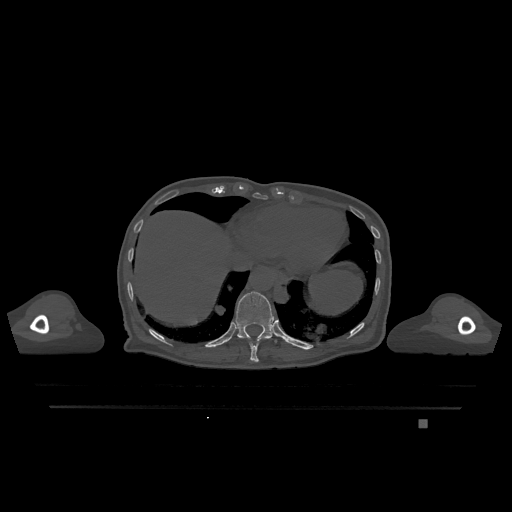
CT including the spine, one axial slice; slice 609 of 1317 in the series (ordered by position); bone window (W 1800 / L 400 HU); 0.5 mm slice thickness; 512 × 512 image matrix. Female patient, age 74 years. From the clinical record (not read from this slice): primary cancer: lung.
Structures marked on this image (semi-automatic segmentation, software-assisted and operator-edited):
- T10 vertebra: box from (x=249, y=338) to (x=266, y=362) px
- T11 vertebra: (x=228, y=291)–(x=277, y=343)